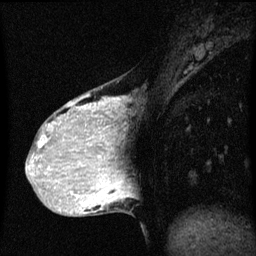
Breast MRI (dynamic contrast-enhanced), one sagittal slice; position 19 of 60 along the scan axis; dynamic contrast-enhanced series, image 2 of 3 at this slice position (ordered by acquisition); 1.5 T; TE 4.2 ms, TR 8 ms; 2 mm slice thickness; 256 × 256 image matrix, field of view 200 × 200 mm. Female patient, age 36 years.
Annotated regions visible in this slice (semi-automatically segmented with operator editing):
- analysis volume of interest (the breast-tissue region the enhancement analysis was run in; not a lesion): box from (x=33, y=82) to (x=119, y=169) px
- tumour enhancement mask (voxels above the 70 % enhancement threshold inside the analysis volume of interest): (x=38, y=98)–(x=119, y=169)